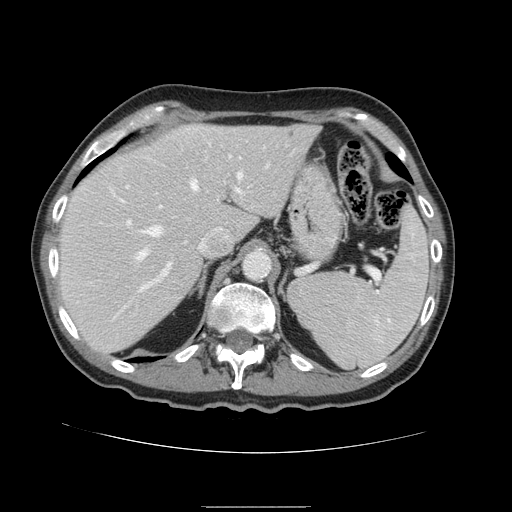
Contrast-enhanced abdominal CT, one axial slice; position 110 of 168 along the scan axis; intravenous contrast given; soft-tissue window (W 400 / L 40 HU); 2.5 mm slice thickness; 512 × 512 image matrix, field of view 386 × 386 mm. Male patient, age 74 years. Case-level facts recorded for this patient, not image findings: diagnosis: colorectal cancer liver metastases, imaged before liver resection; multiple liver metastases: no; largest metastasis: 14.5 cm; disease in both lobes: yes.
Annotated regions visible in this slice (outlined manually by an expert reader):
- hepatic veins: bounding box (x1, y1, x2, y2) in pixels: (139, 173, 242, 258)
- liver: (59, 125, 320, 353)
- planned liver remnant (the part of the liver to remain after resection): (59, 125, 321, 353)
- portal vein (with intrahepatic branches): (94, 189, 244, 292)